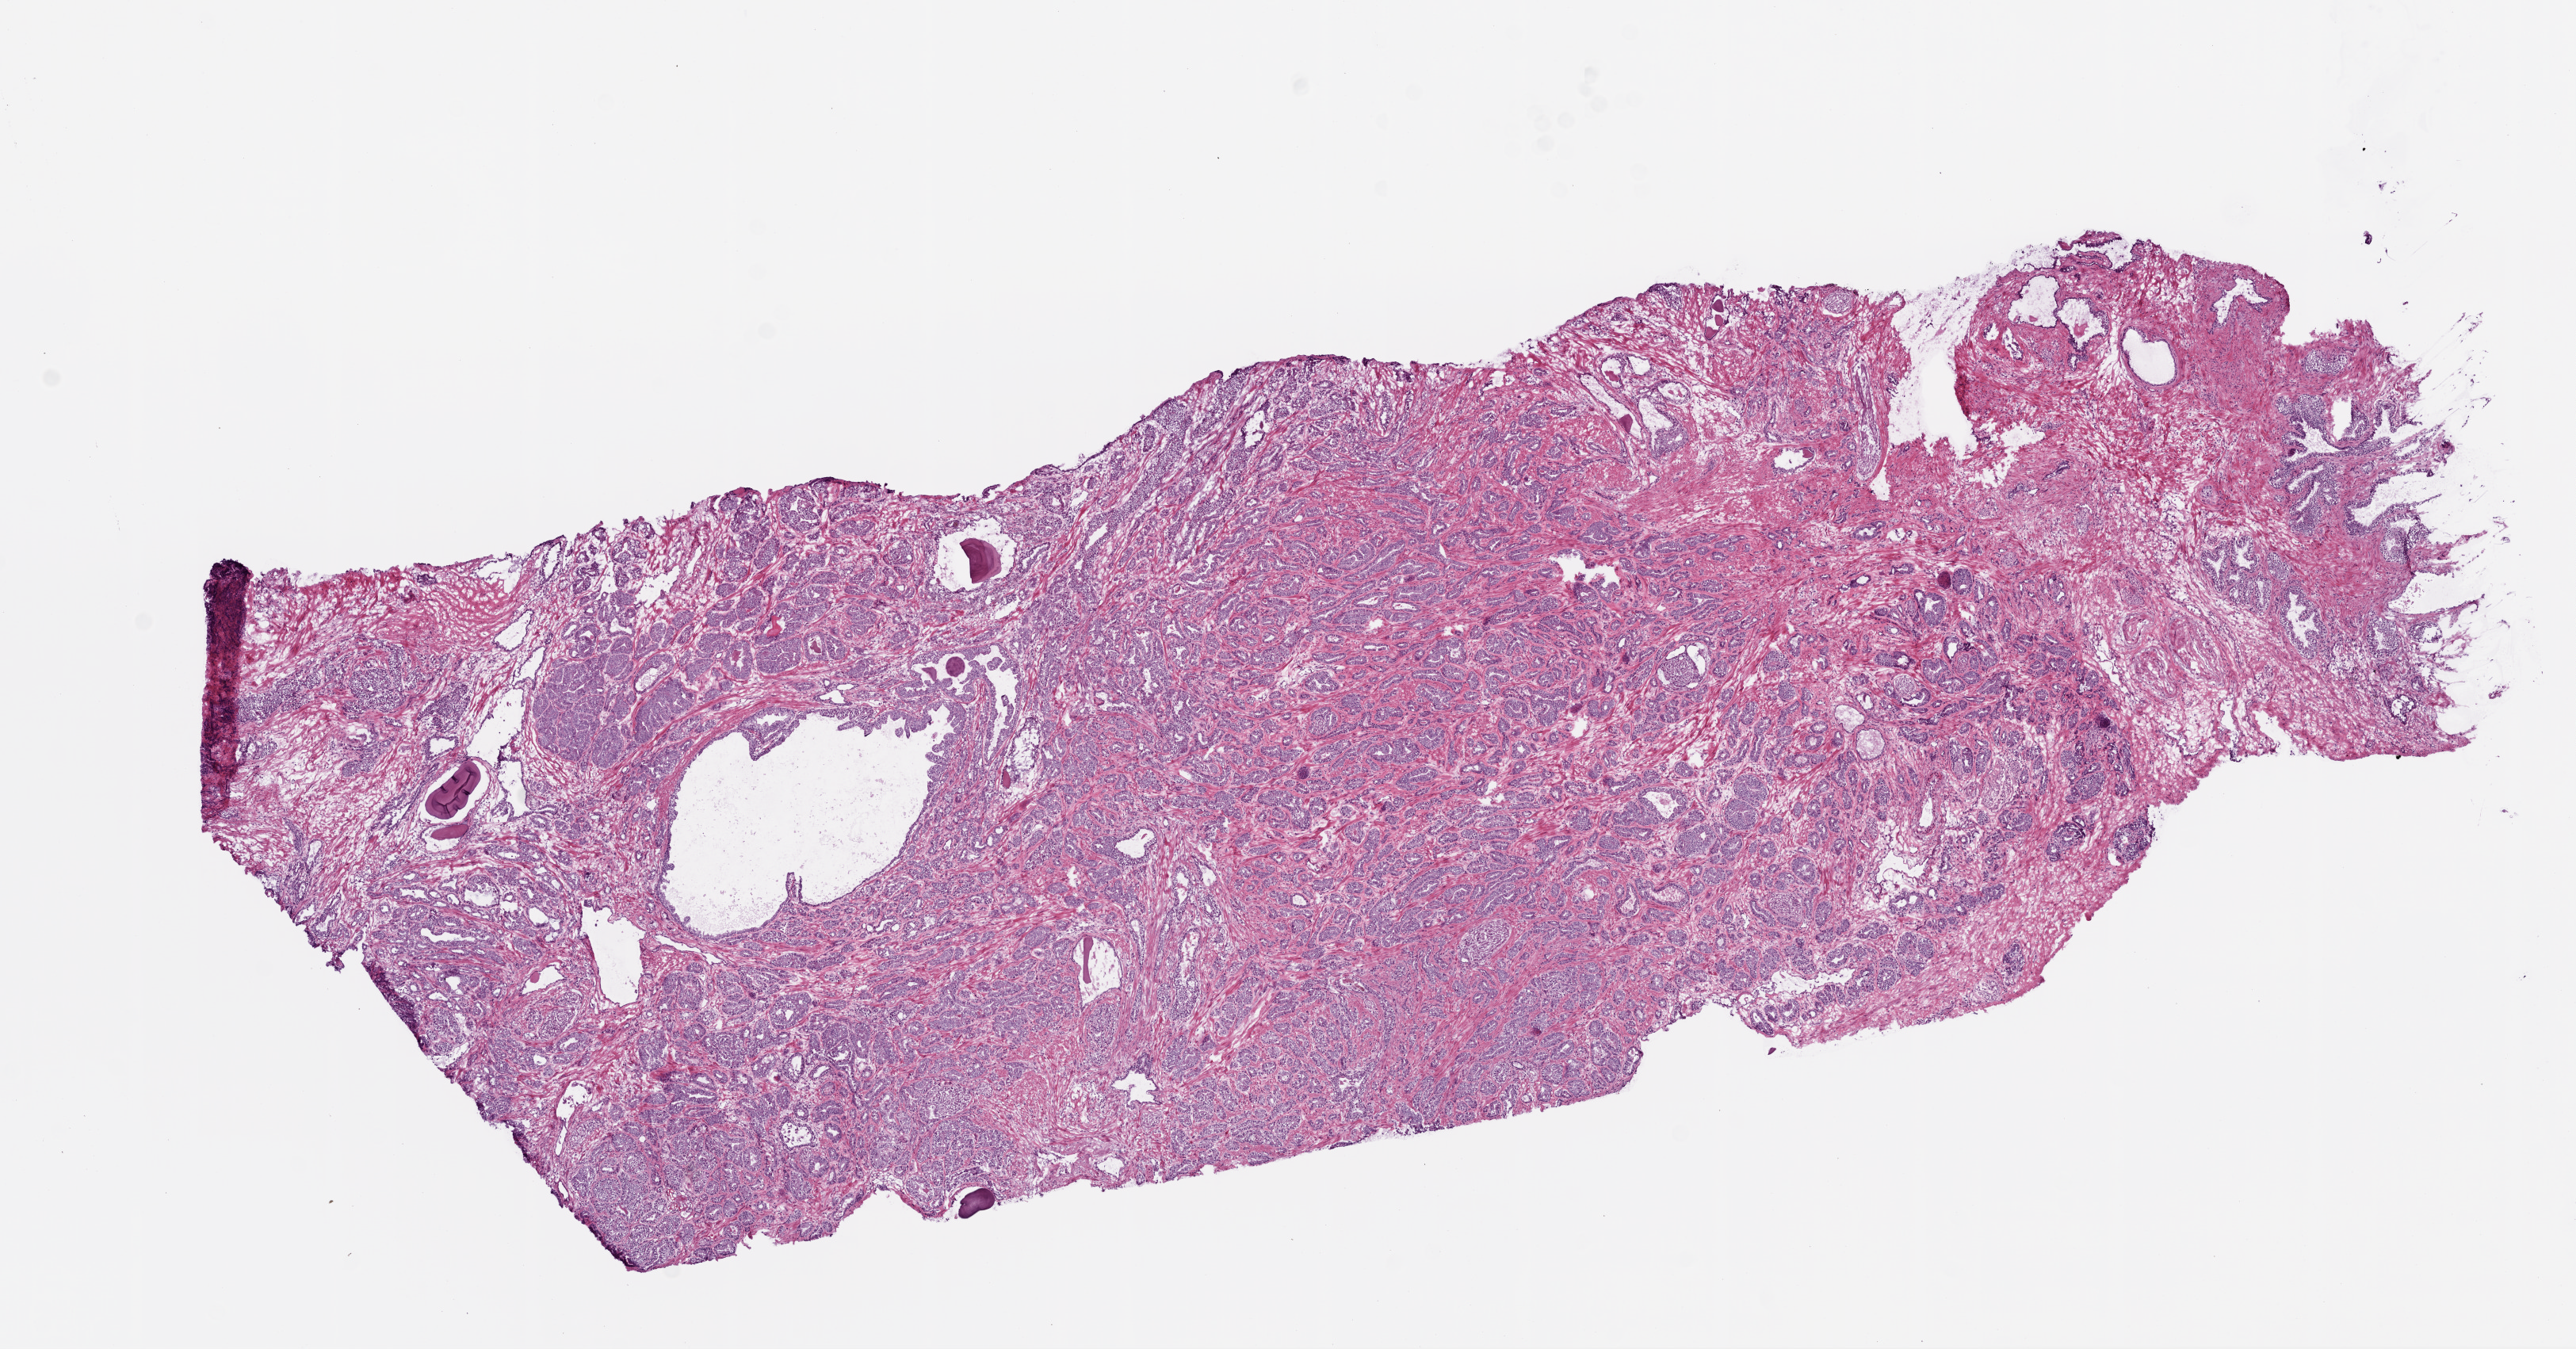
H&E-stained whole-slide image — a low-resolution overview of the entire scanned area, about 13.0 x 6.8 mm; frozen section from the top of the tissue portion; primary tumour sample from the prostate. Male, age 66 years at initial diagnosis. Gleason score: 7 (3+4). Composition of this section per pathologist review: tumour cells 65%, tumour nuclei 70%, normal cells 20%, stromal cells 15%, necrosis 0%. Inflammatory infiltration, as recorded: lymphocyte infiltration 0%, monocyte infiltration 0%, neutrophil infiltration 0%.
Pathologic diagnosis: Acinar cell carcinoma (prostate gland). Lymph nodes positive (case pathology): 0 of 5 examined.